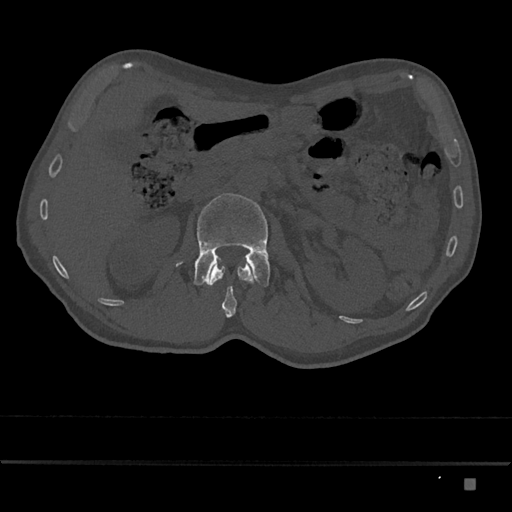
CT including the spine, one axial slice. Slice 502 of 797 in the series (ordered by position). 120 kVp. Bone window (W 1800 / L 400 HU). 0.5 mm slice thickness. 512 × 512 image matrix. Male patient, age 72 years. Case-level facts recorded for this patient, not image findings: primary cancer: prostate.
Annotated regions visible in this slice (semi-automatic segmentation, software-assisted and operator-edited):
- L1 vertebra: box from (x=206, y=260) to (x=255, y=318) px
- L2 vertebra: (x=176, y=193)–(x=270, y=287)